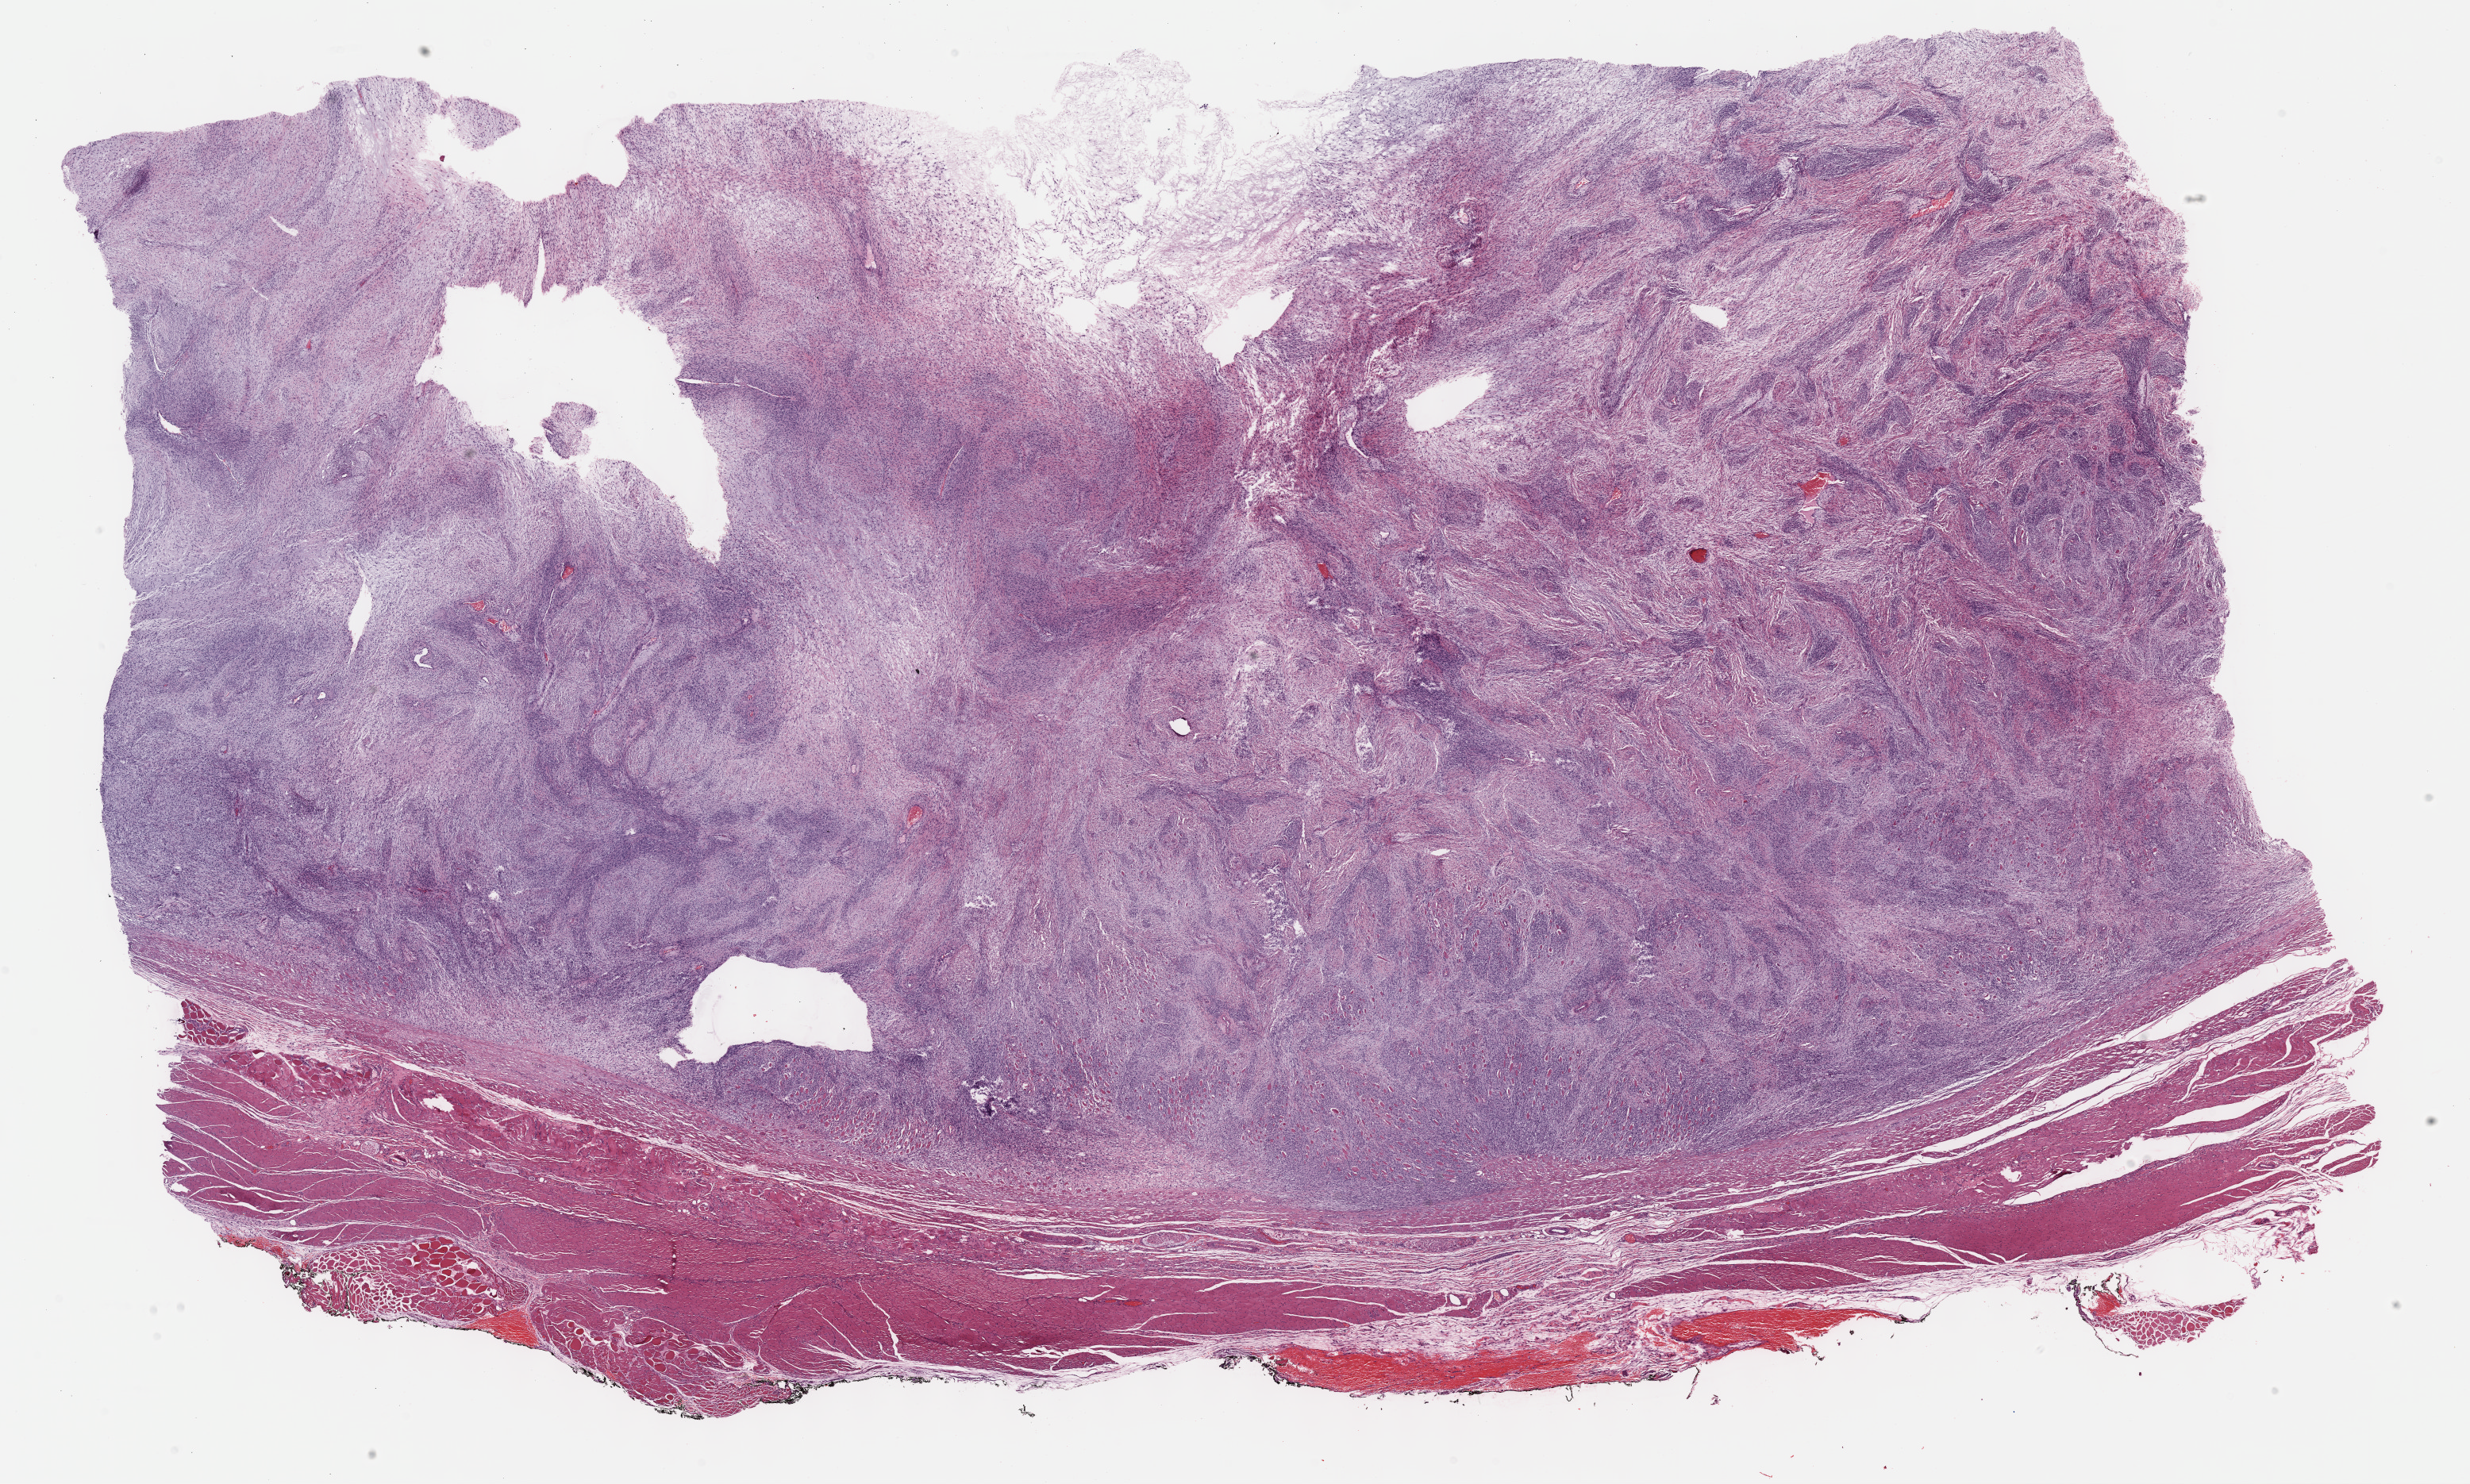
Digitized H&E tissue section (whole slide) — a low-resolution overview of the entire scanned area, about 25.2 x 15.1 mm (slide scanned at 40x), formalin-fixed paraffin-embedded (FFPE) diagnostic section, connective, subcutaneous and other soft tissues, primary tumour sample. Patient: female, age at initial diagnosis 53 years.
* diagnosis: Fibromyxosarcoma (connective, subcutaneous and other soft tissues of lower limb and hip)